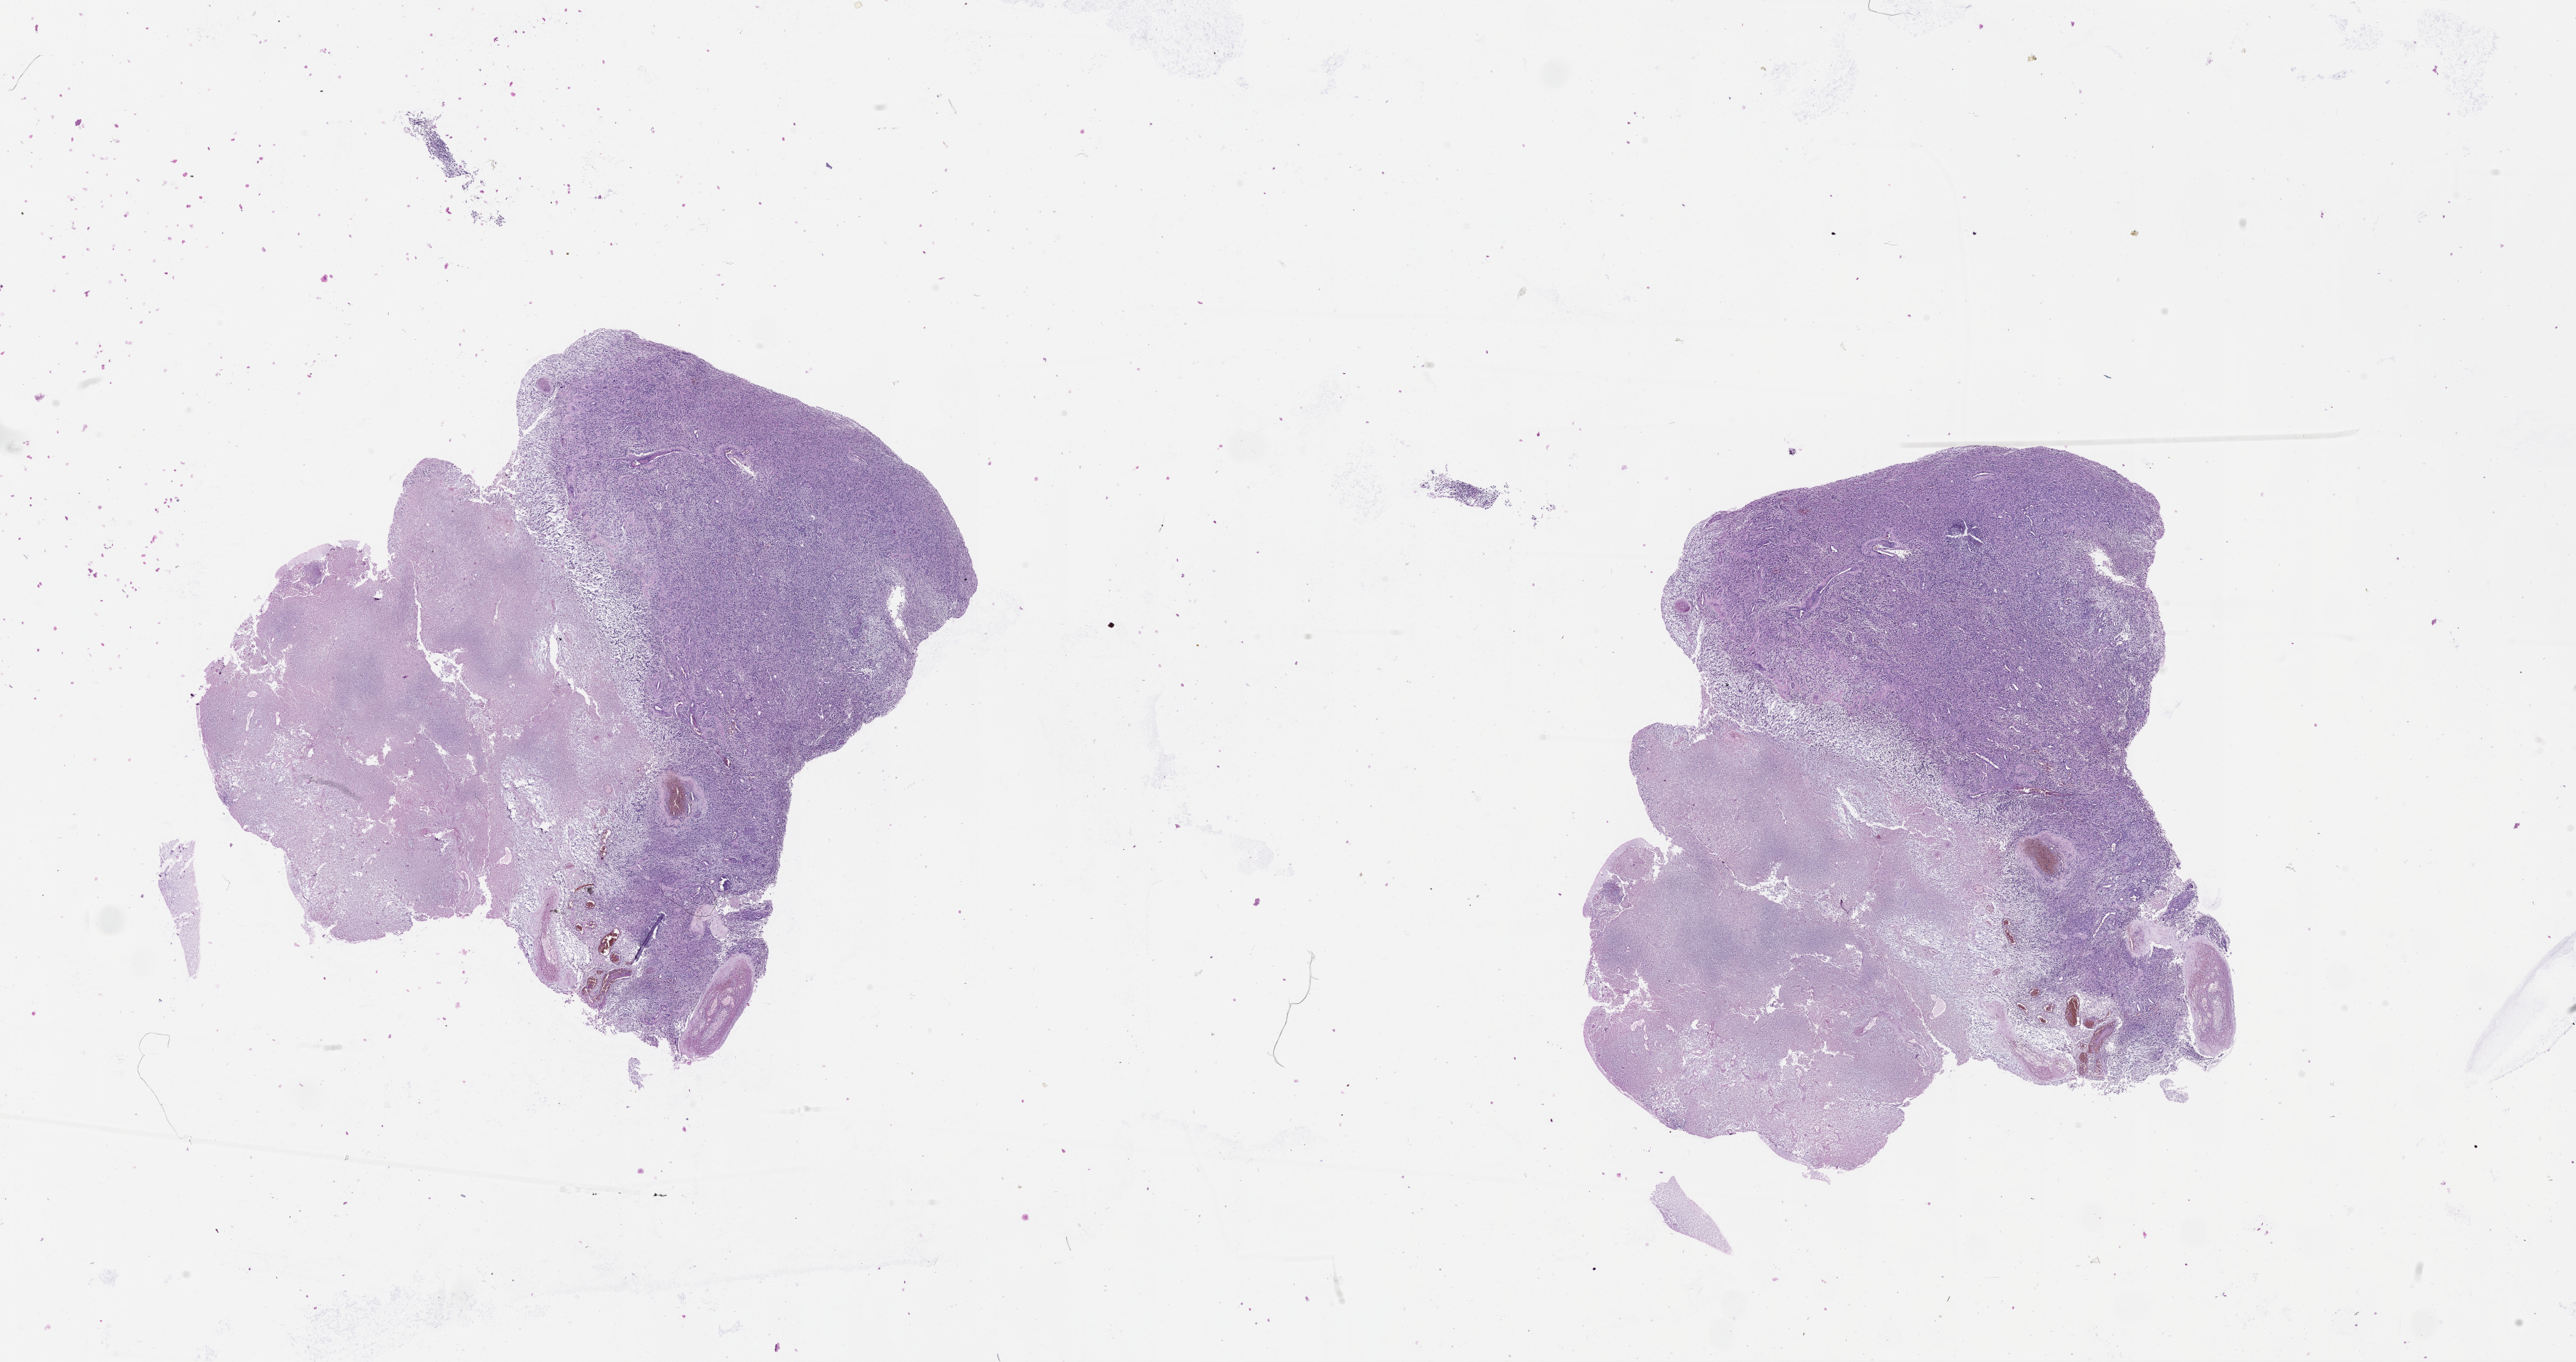
H&E-stained whole-slide image, low-resolution overview of the scanned area, about 29.1 x 15.4 mm, brain, tumour tissue. Patient: male, age 65 years.
Primary tumour site (as recorded): parietal lobe. Diagnosis: Glioblastoma.